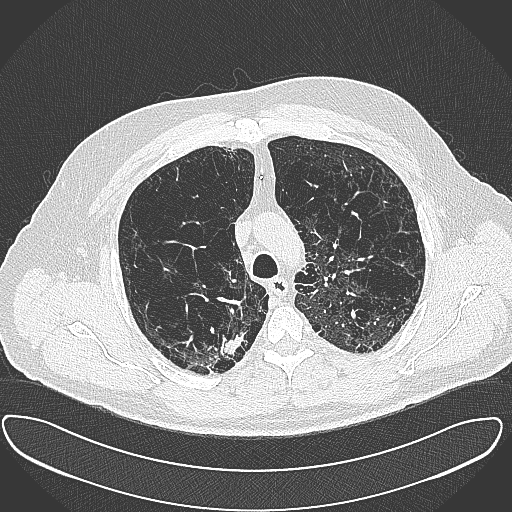
Axial slice from a low-dose chest CT screening exam. First (baseline) screen. Lung window (W 1500 / L -600 HU). 1 mm slice thickness. Slice 93 of 385 in the series. 512 × 512 image matrix. Male participant, aged 60 years at enrolment. Current smoker at enrolment.
Expert reader's lesion annotation, bounding box [x1, y1, x2, y2] px = [193, 327, 250, 377]. Reader record for this screening exam (exam-level; its link to the box is not recorded): non-calcified nodule or mass ≥4 mm, right upper lobe, 15 × 25 mm, spiculated (stellate) margins, soft tissue attenuation.